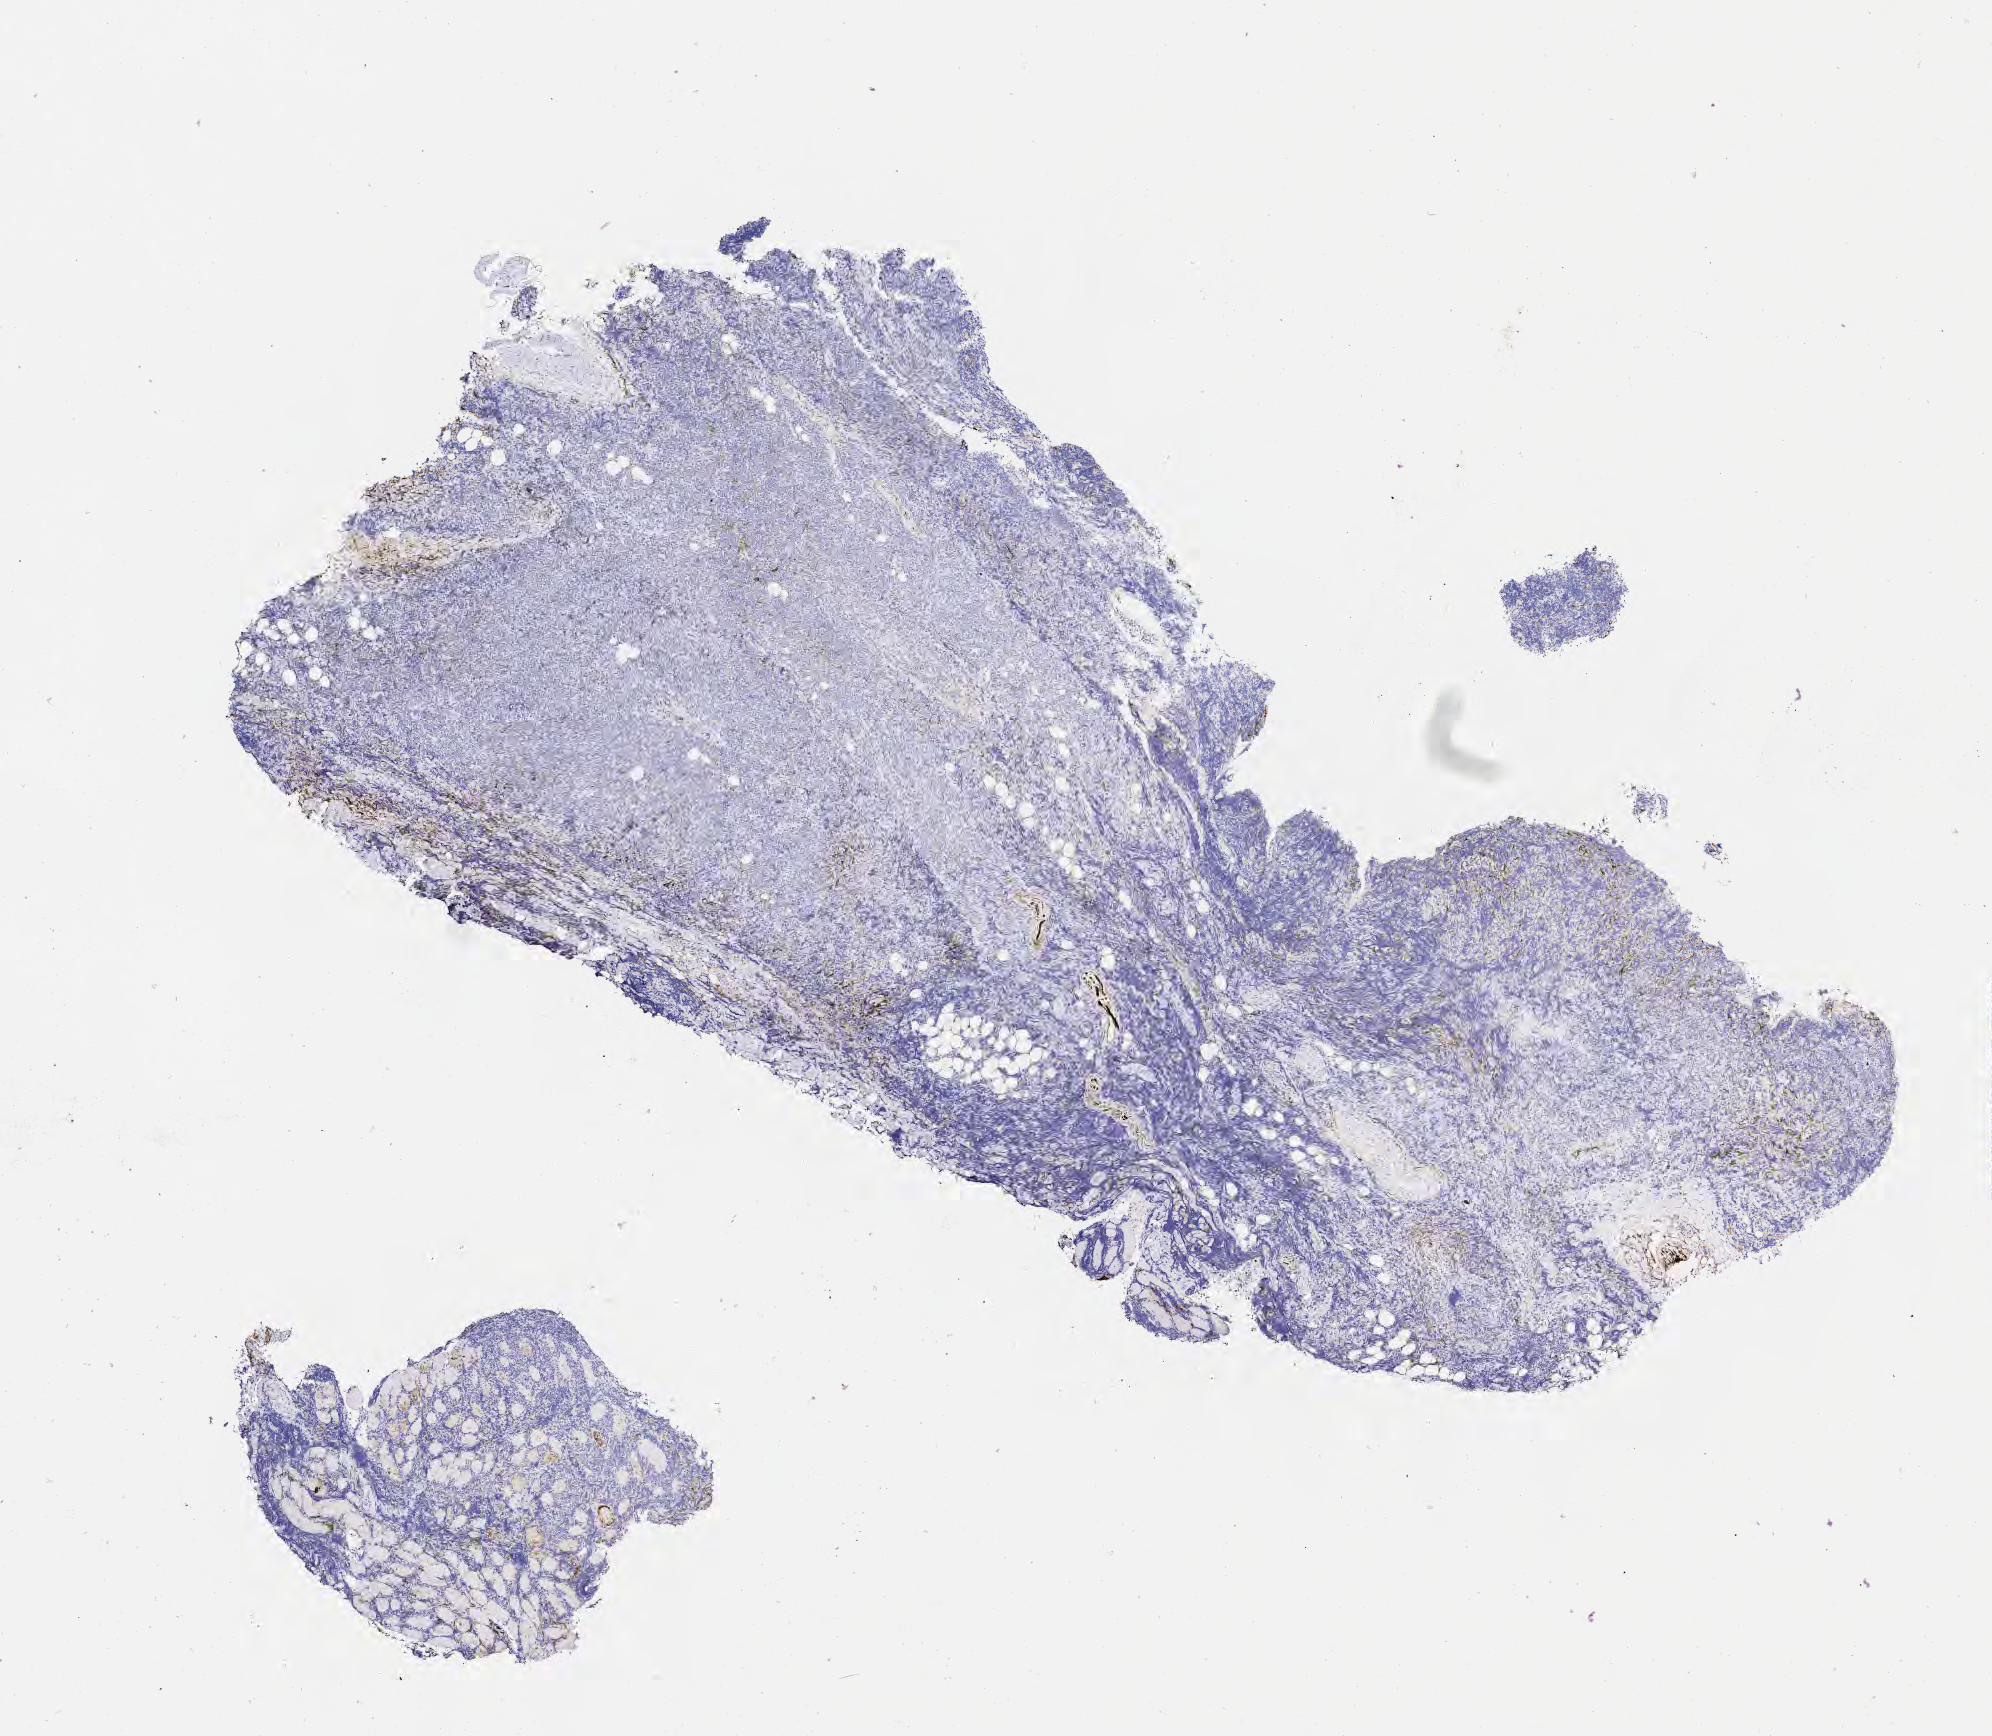
Whole-slide image, immunohistochemical stain for CD10, whole scanned area (about 8.0 x 7.0 mm) shown as a low-resolution overview; specimen: tumor tissue. Patient: male, aged 67.
* histologic diagnosis: Diffuse large B-cell lymphoma, NOS